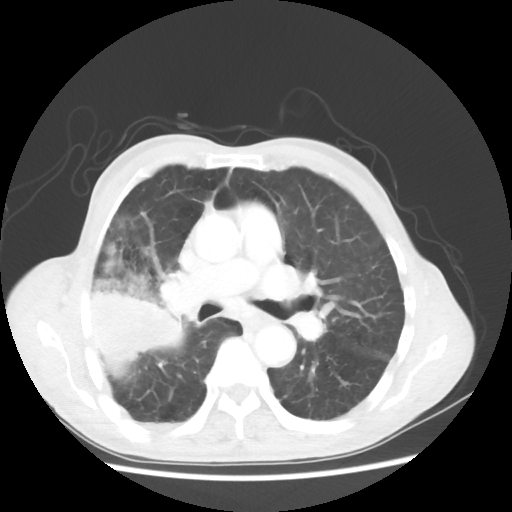
Chest CT, one axial slice. Slice 32 of 58 in the series (ordered by position). Reconstruction kernel STANDARD. 100 kVp. Lung window (W 1500 / L -600 HU). 512 × 512 image matrix, field of view 351 × 351 mm. Patient: male, 75 years. Case-level facts recorded for this patient, not image findings: clinical TNM (as recorded): T4 N1 M1.
Annotated regions visible in this slice (rectangle marked by the reading radiologist):
- lung tumour (recorded histology: adenocarcinoma): bounding box [x1, y1, x2, y2] px = [78, 266, 190, 380]